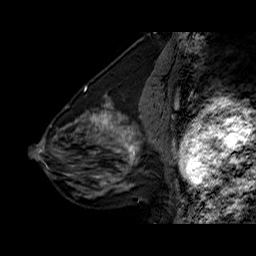
Breast MRI (dynamic contrast-enhanced), one sagittal slice. Slice 26 of 60 in the series (ordered by position). Dynamic contrast-enhanced series, time point 2 of 6 at this slice position (early post-contrast). 1.5 T. TE 6.3 ms, TR 32.5 ms. 4 mm slice thickness. 256 × 256 image matrix, field of view 200 × 200 mm. Female patient. Case-level facts recorded for this patient, not image findings: setting: breast cancer imaged before/during neoadjuvant chemotherapy; receptor status: triple-negative.
Structures marked on this image (semi-automatic segmentation, software-assisted and operator-edited):
- analysis volume of interest (the breast-tissue region the enhancement analysis was run in; not a lesion): bounding box [x1, y1, x2, y2] px = [108, 126, 154, 177]
- tumour enhancement mask (voxels above the 100 % enhancement threshold inside the analysis volume of interest): [111, 126, 140, 162]